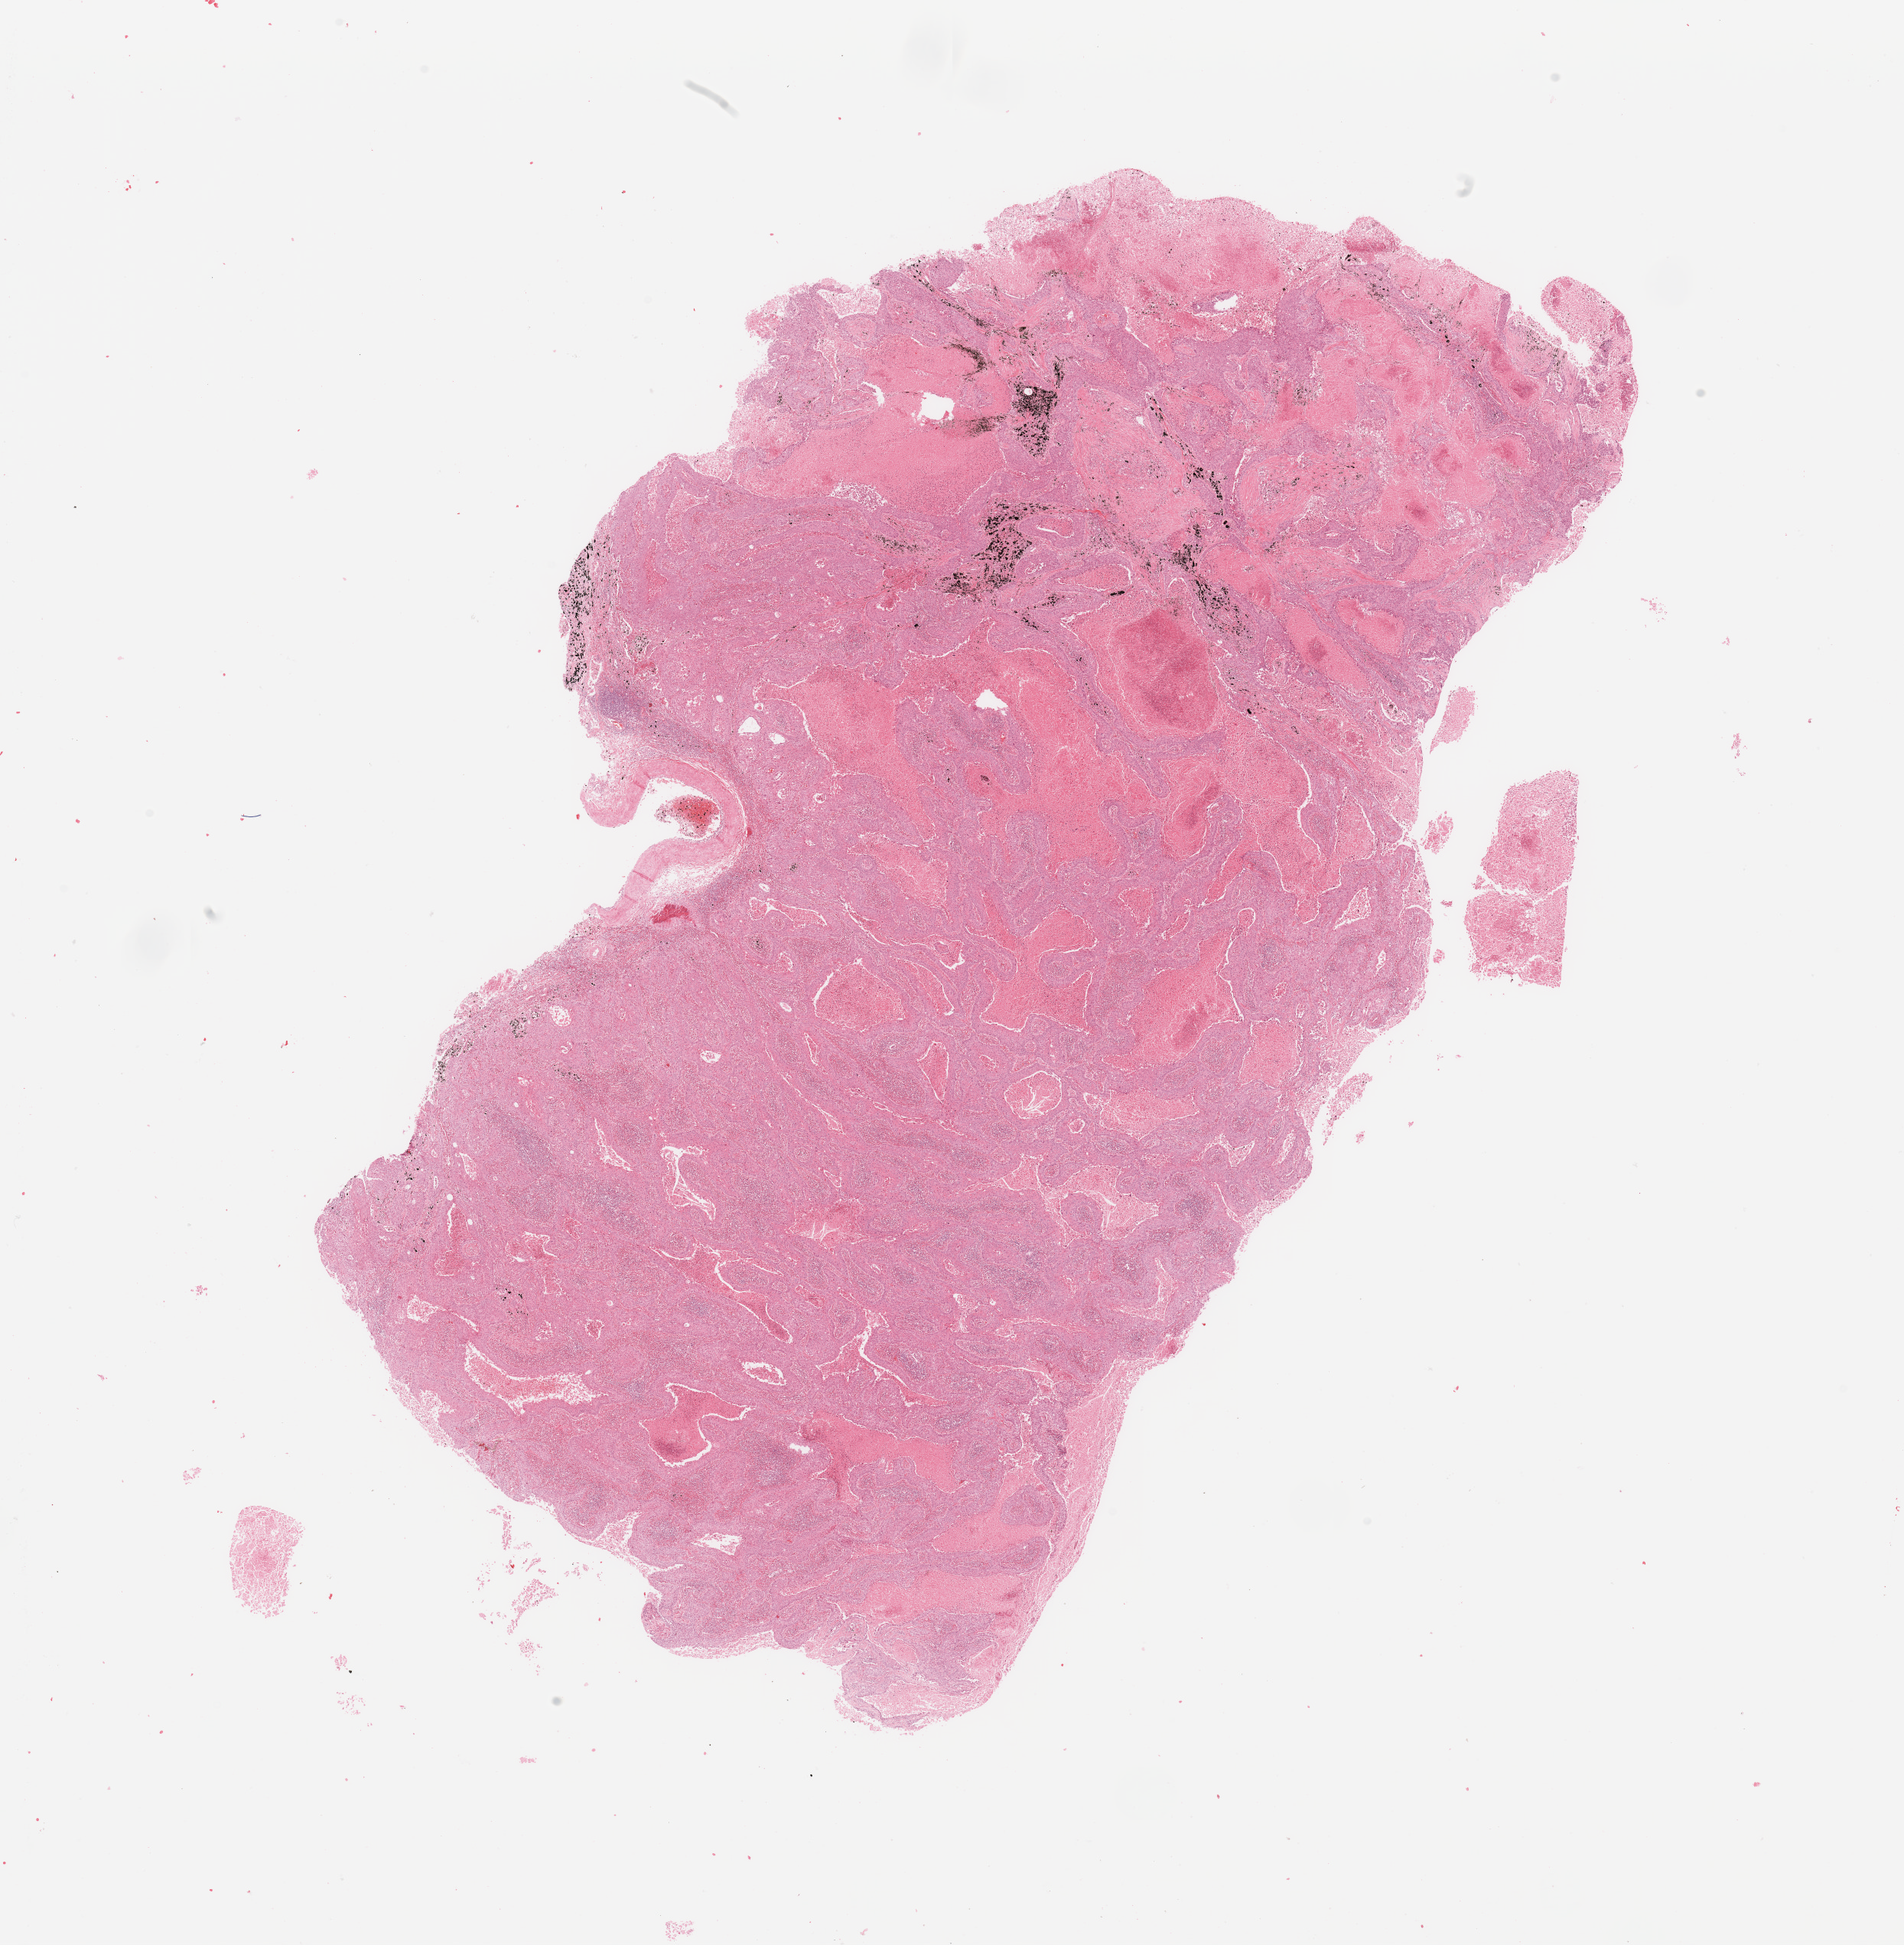
H&E whole-slide image, a low-resolution overview of the entire scanned area, about 19.7 x 20.1 mm (acquisition: 20x scan), lung, tumour tissue. Patient: male, age 56 years.
Diagnosis: Squamous cell carcinoma, NOS.